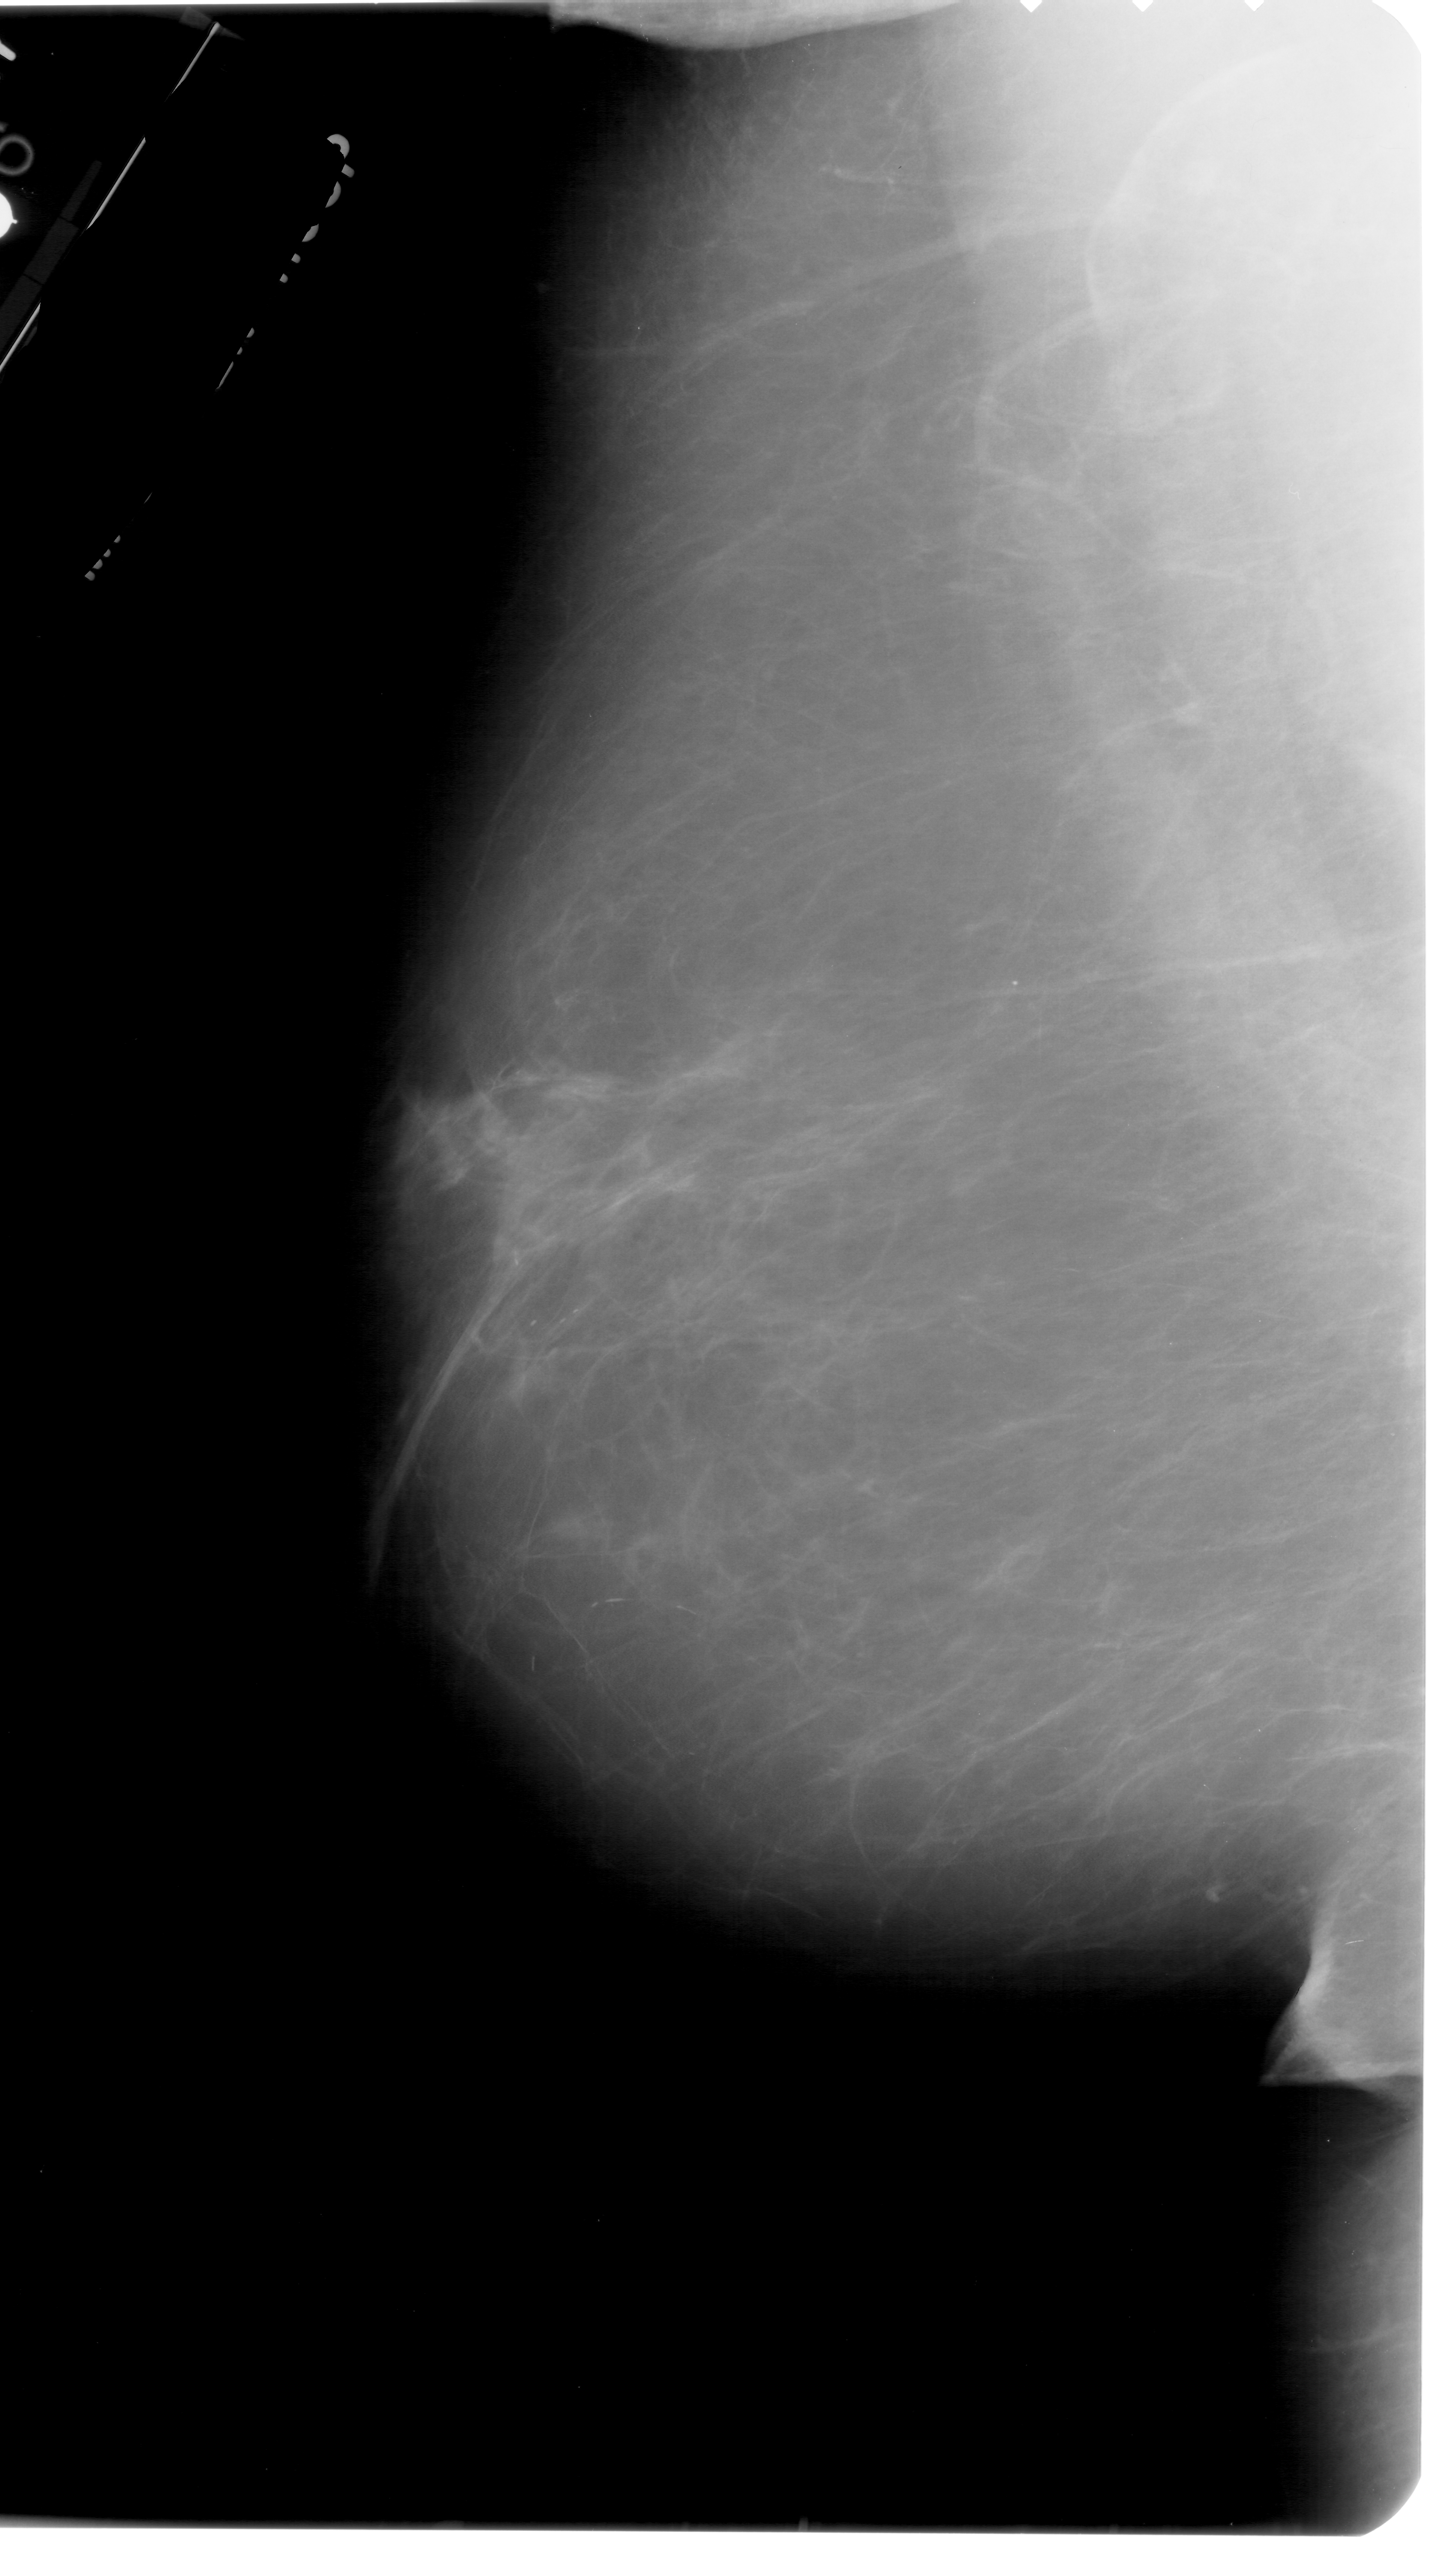
Digitized screen-film mammogram. Left breast. Mediolateral oblique (MLO) view. 1429 × 2576 image matrix.
Marked abnormalities (boxes around the expert regions of interest):
- calcifications, morphology pleomorphic, distribution clustered; BI-RADS assessment category 4; pathology result (as recorded, not read from the image): malignant: box from (x=481, y=985) to (x=632, y=1118) px